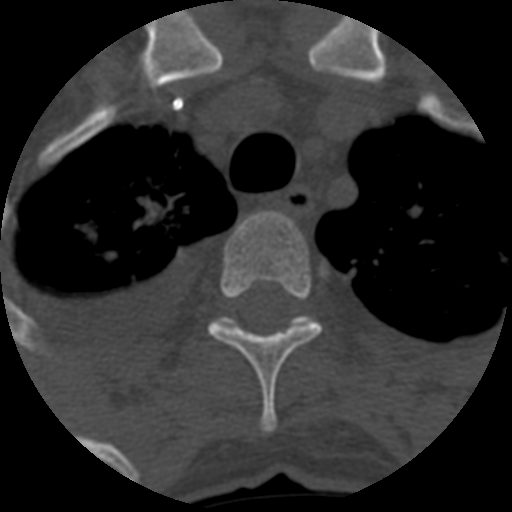
CT including the spine, one axial slice. Slice 486 of 708 in the series (ordered by position). Reconstruction kernel STANDARD. One of 3 acquisitions stored at this slice position. Bone window (W 1800 / L 400 HU). 1.25 mm slice thickness. 512 × 512 image matrix, field of view 160 × 160 mm. Patient age 55 years. Case-level facts recorded for this patient, not image findings: primary cancer: colon; vertebrae with lytic lesions (as recorded): T12, L1, L5.
Outlined on this slice (semi-automatic segmentation, software-assisted and operator-edited):
- T3 vertebra: bounding box (x1, y1, x2, y2) in pixels: (208, 212, 323, 433)
- T4 vertebra: (214, 316, 318, 335)